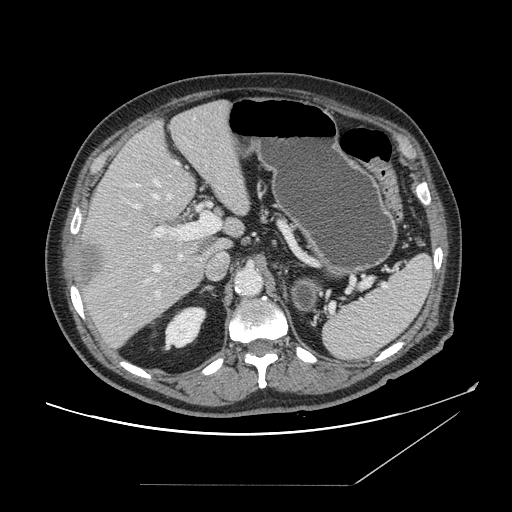
Contrast-enhanced abdominal CT, one axial slice. Slice 100 of 166 in the series (ordered by position). Intravenous contrast given. Soft-tissue window (W 400 / L 40 HU). 2.5 mm slice thickness. 512 × 512 image matrix. Male patient, age 80 years. From the clinical record (not read from this slice): diagnosis: colorectal cancer liver metastases, imaged before liver resection; multiple liver metastases: no; largest metastasis: 2.2 cm.
Outlined on this slice (outlined manually by an expert reader):
- hepatic veins: bounding box <145,180,172,284> (left, top, right, bottom; pixels)
- liver: <79,102,251,349>
- planned liver remnant (the part of the liver to remain after resection): <90,101,250,256>
- portal vein (with intrahepatic branches): <136,206,221,297>
- liver metastasis: <84,243,104,285>